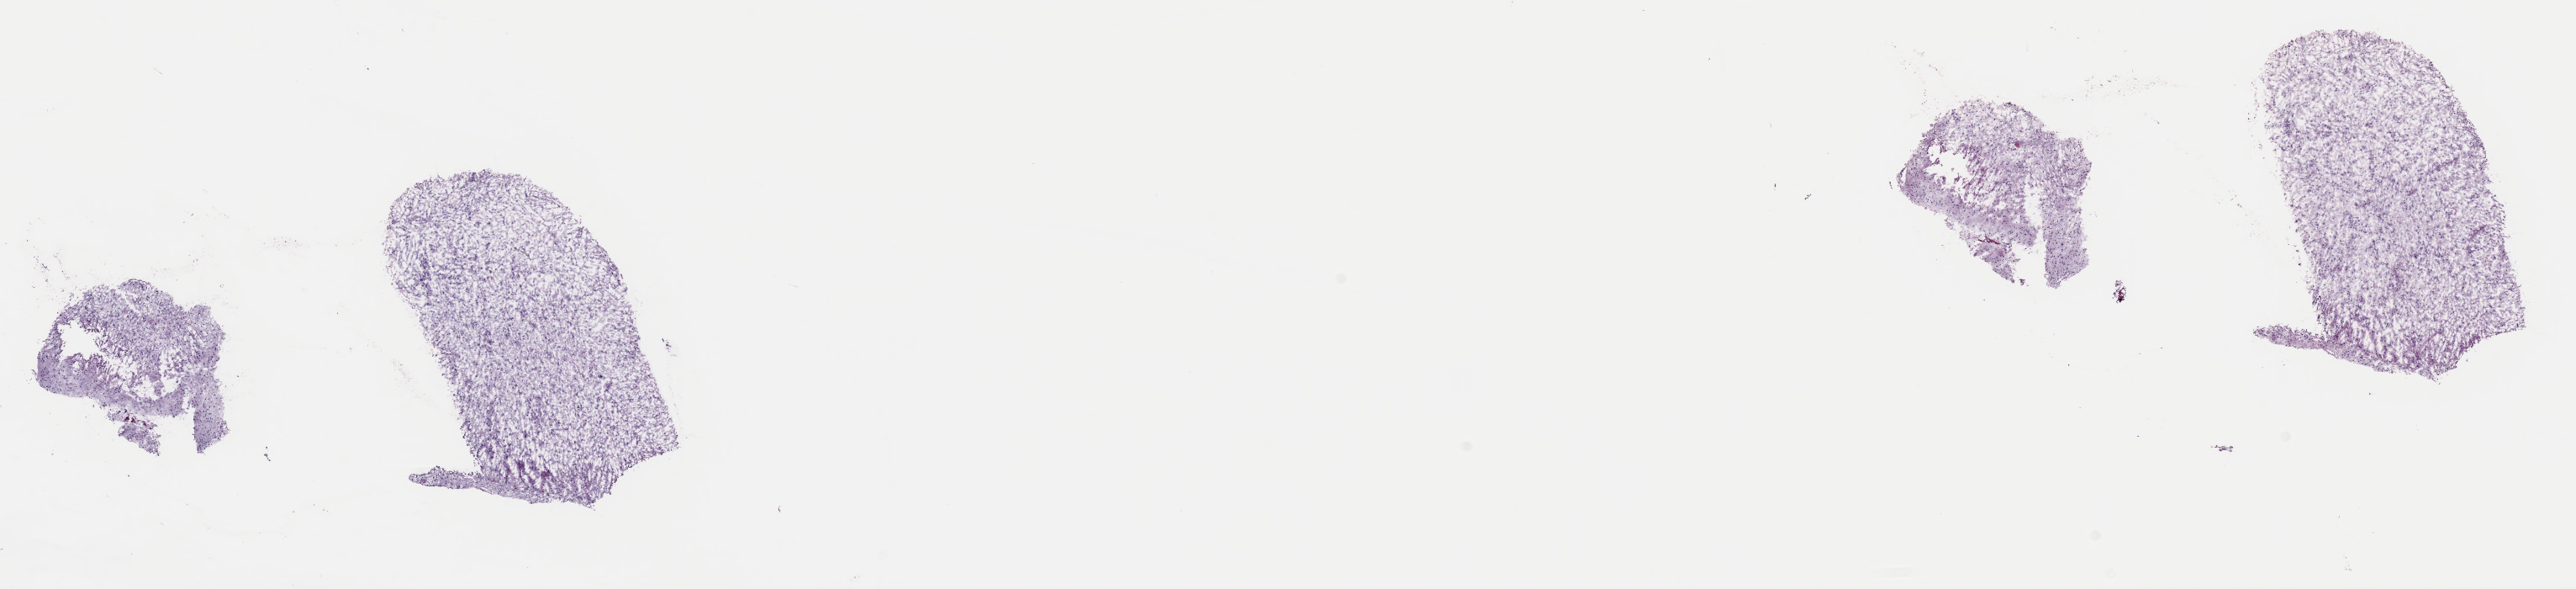
Whole-slide histology image, H&E, shown as a low-resolution overview of the whole scanned area (about 24.2 x 5.5 mm), frozen section from the top of the tissue portion, primary tumour sample from the brain. Patient: male, age at initial diagnosis 43 years. Histologic grade: G3 (poorly differentiated). Pathologist review of this section (percent, as recorded): tumour cells 60%, tumour nuclei 85%, normal cells 10%, stromal cells 30%, necrosis 0%. Inflammatory infiltration, as recorded: lymphocyte infiltration 0%, monocyte infiltration 0%, neutrophil infiltration 0%.
Laterality: right. Histologic diagnosis: Mixed glioma (cerebrum).